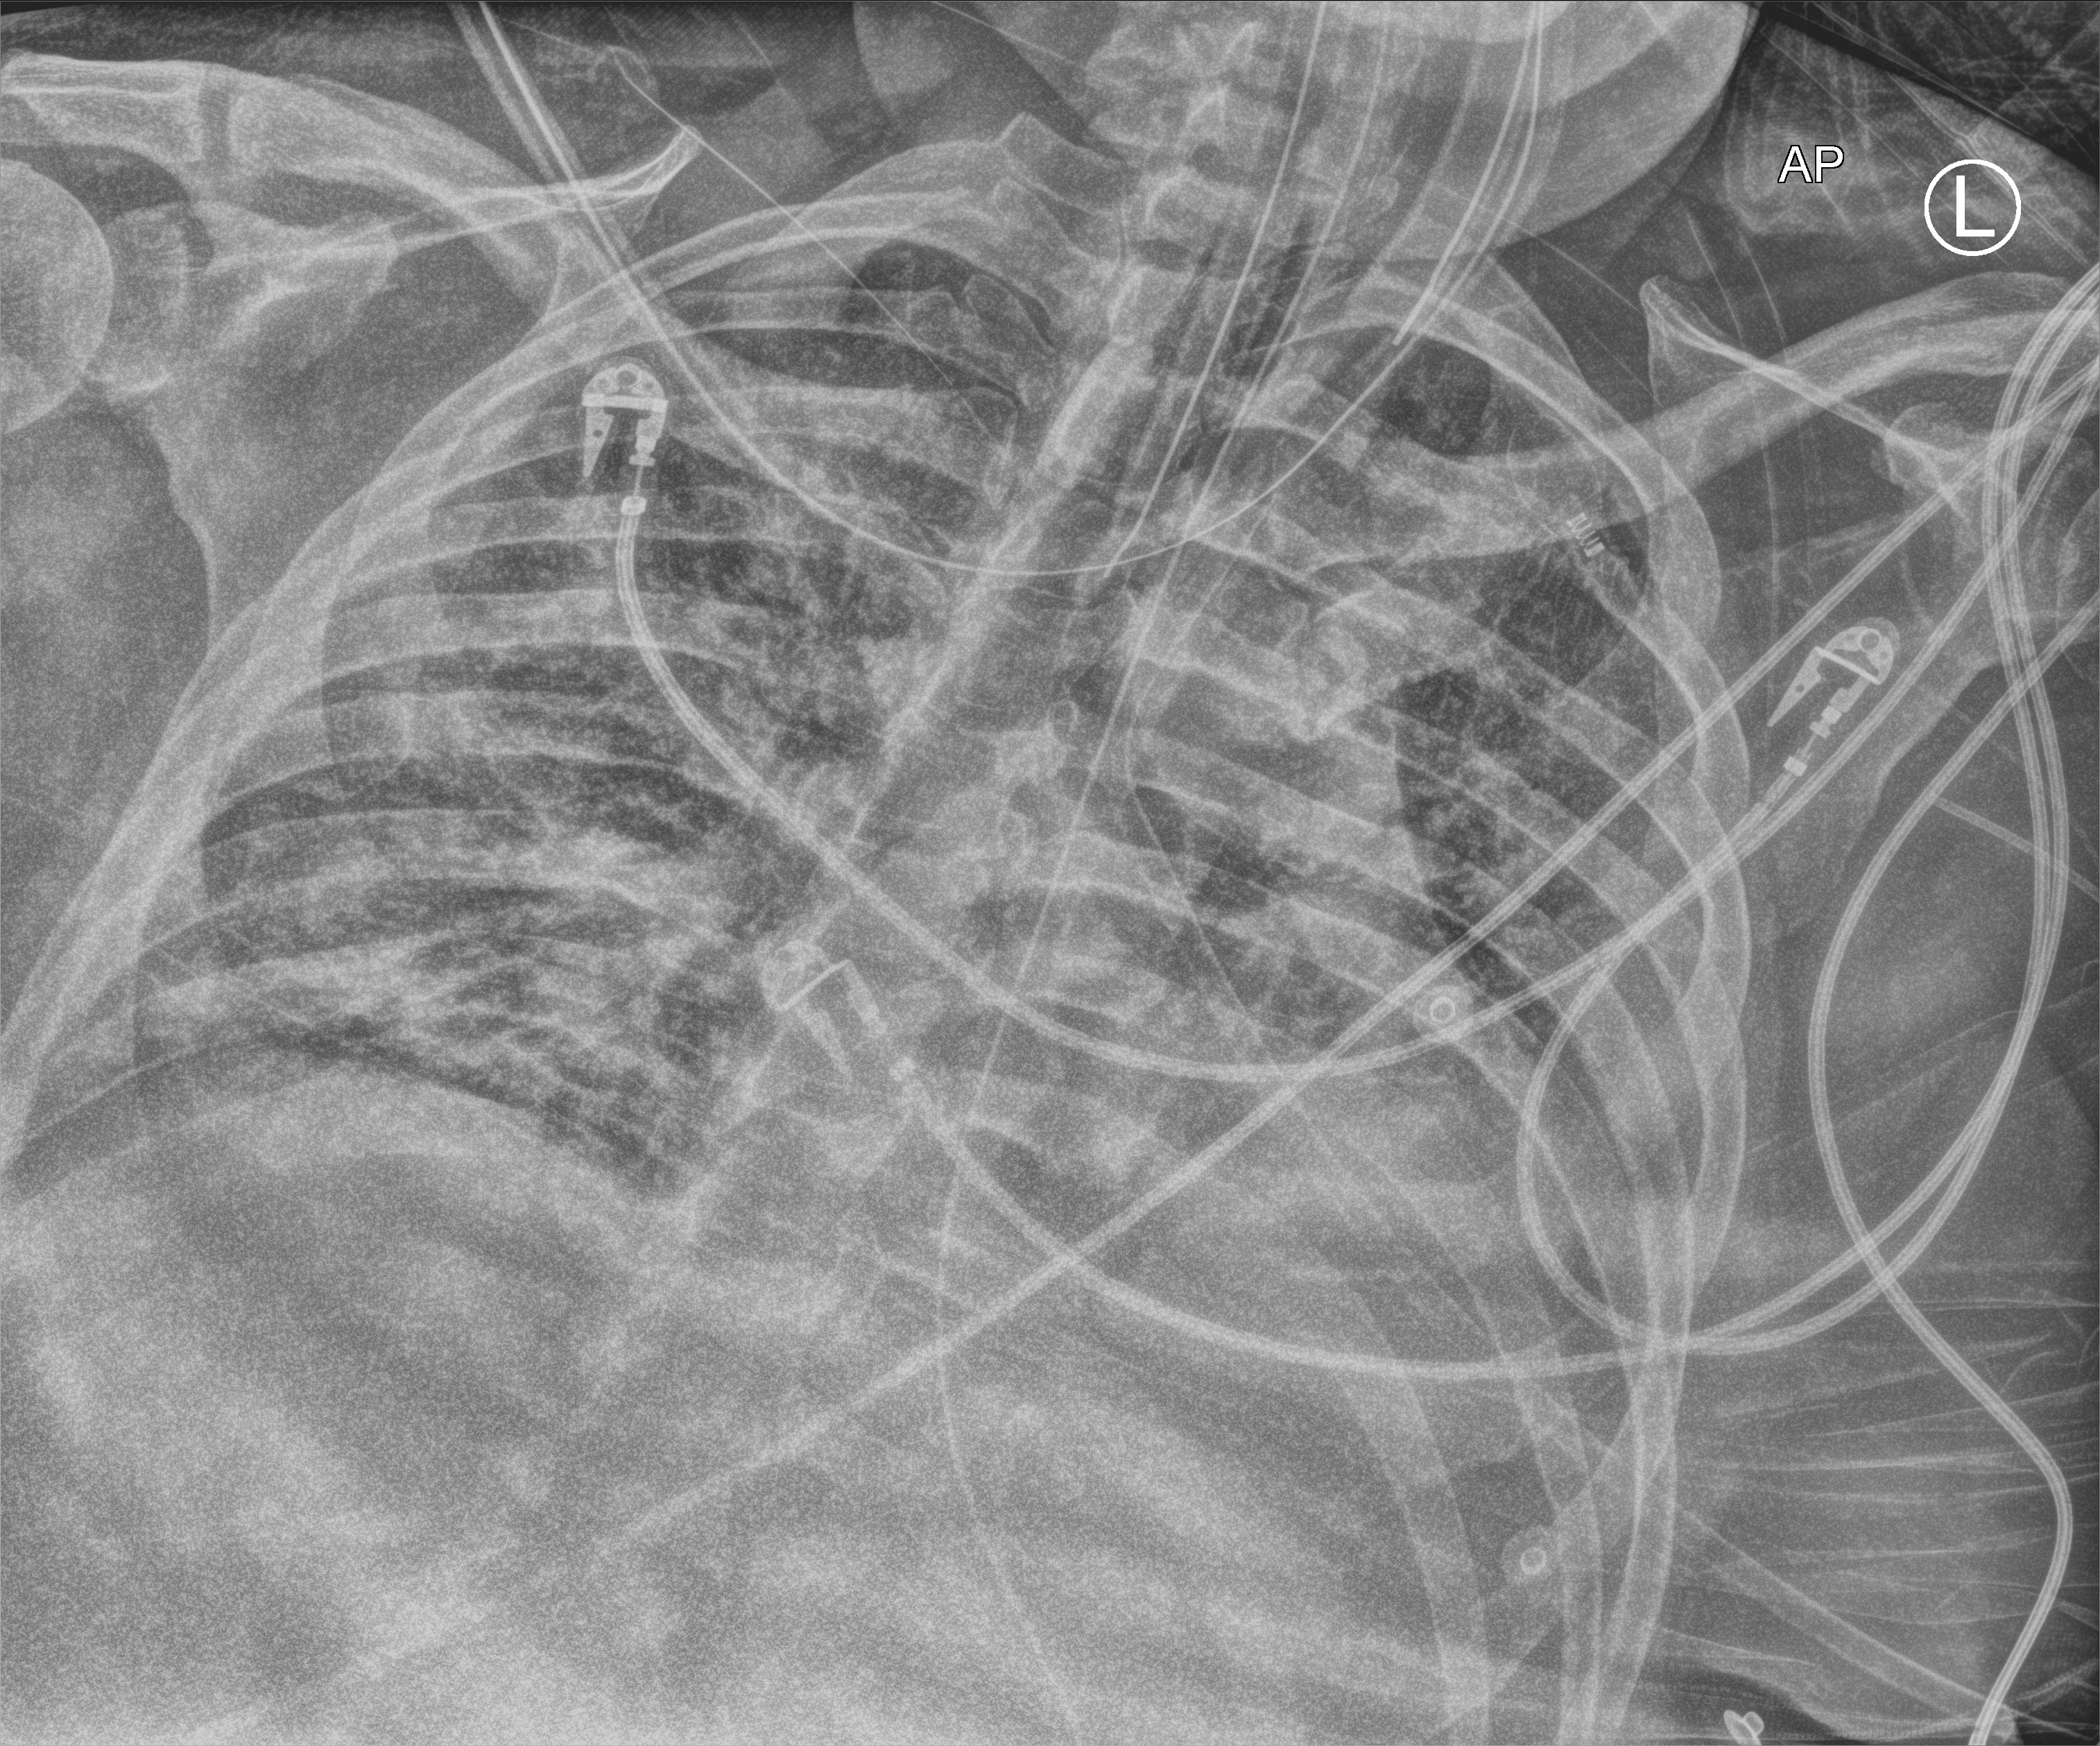
Portable chest radiograph, anteroposterior (AP) projection. Male patient hospitalised with COVID-19, age 18–59 years.
Admission-level facts for this patient (not findings on this image; timing relative to this image not recorded): mechanically ventilated during this hospital stay: yes; hypertension (admission record): yes.